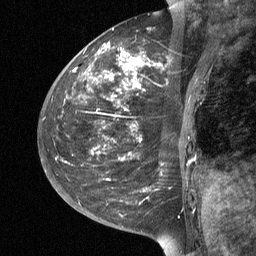
Breast MRI (dynamic contrast-enhanced), one sagittal slice. Position 18 of 64 along the scan axis. Dynamic contrast-enhanced study with each time point stored as its own series, time point 2 of 3 at this slice position (early post-contrast, ordered by acquisition time). 1.5 T. TE 4.8 ms, TR 27 ms. 256 × 256 image matrix. Patient: female, 42 years. Case-level facts recorded for this patient, not image findings: setting: breast cancer imaged before/during neoadjuvant chemotherapy; receptor status: triple-negative.
Outlined on this slice (semi-automatically segmented with operator editing):
- analysis volume of interest (the breast-tissue region the enhancement analysis was run in; not a lesion): bounding box <43,29,203,190> (left, top, right, bottom; pixels)
- tumour enhancement mask (voxels above the 90 % enhancement threshold inside the analysis volume of interest): <75,45,158,160>